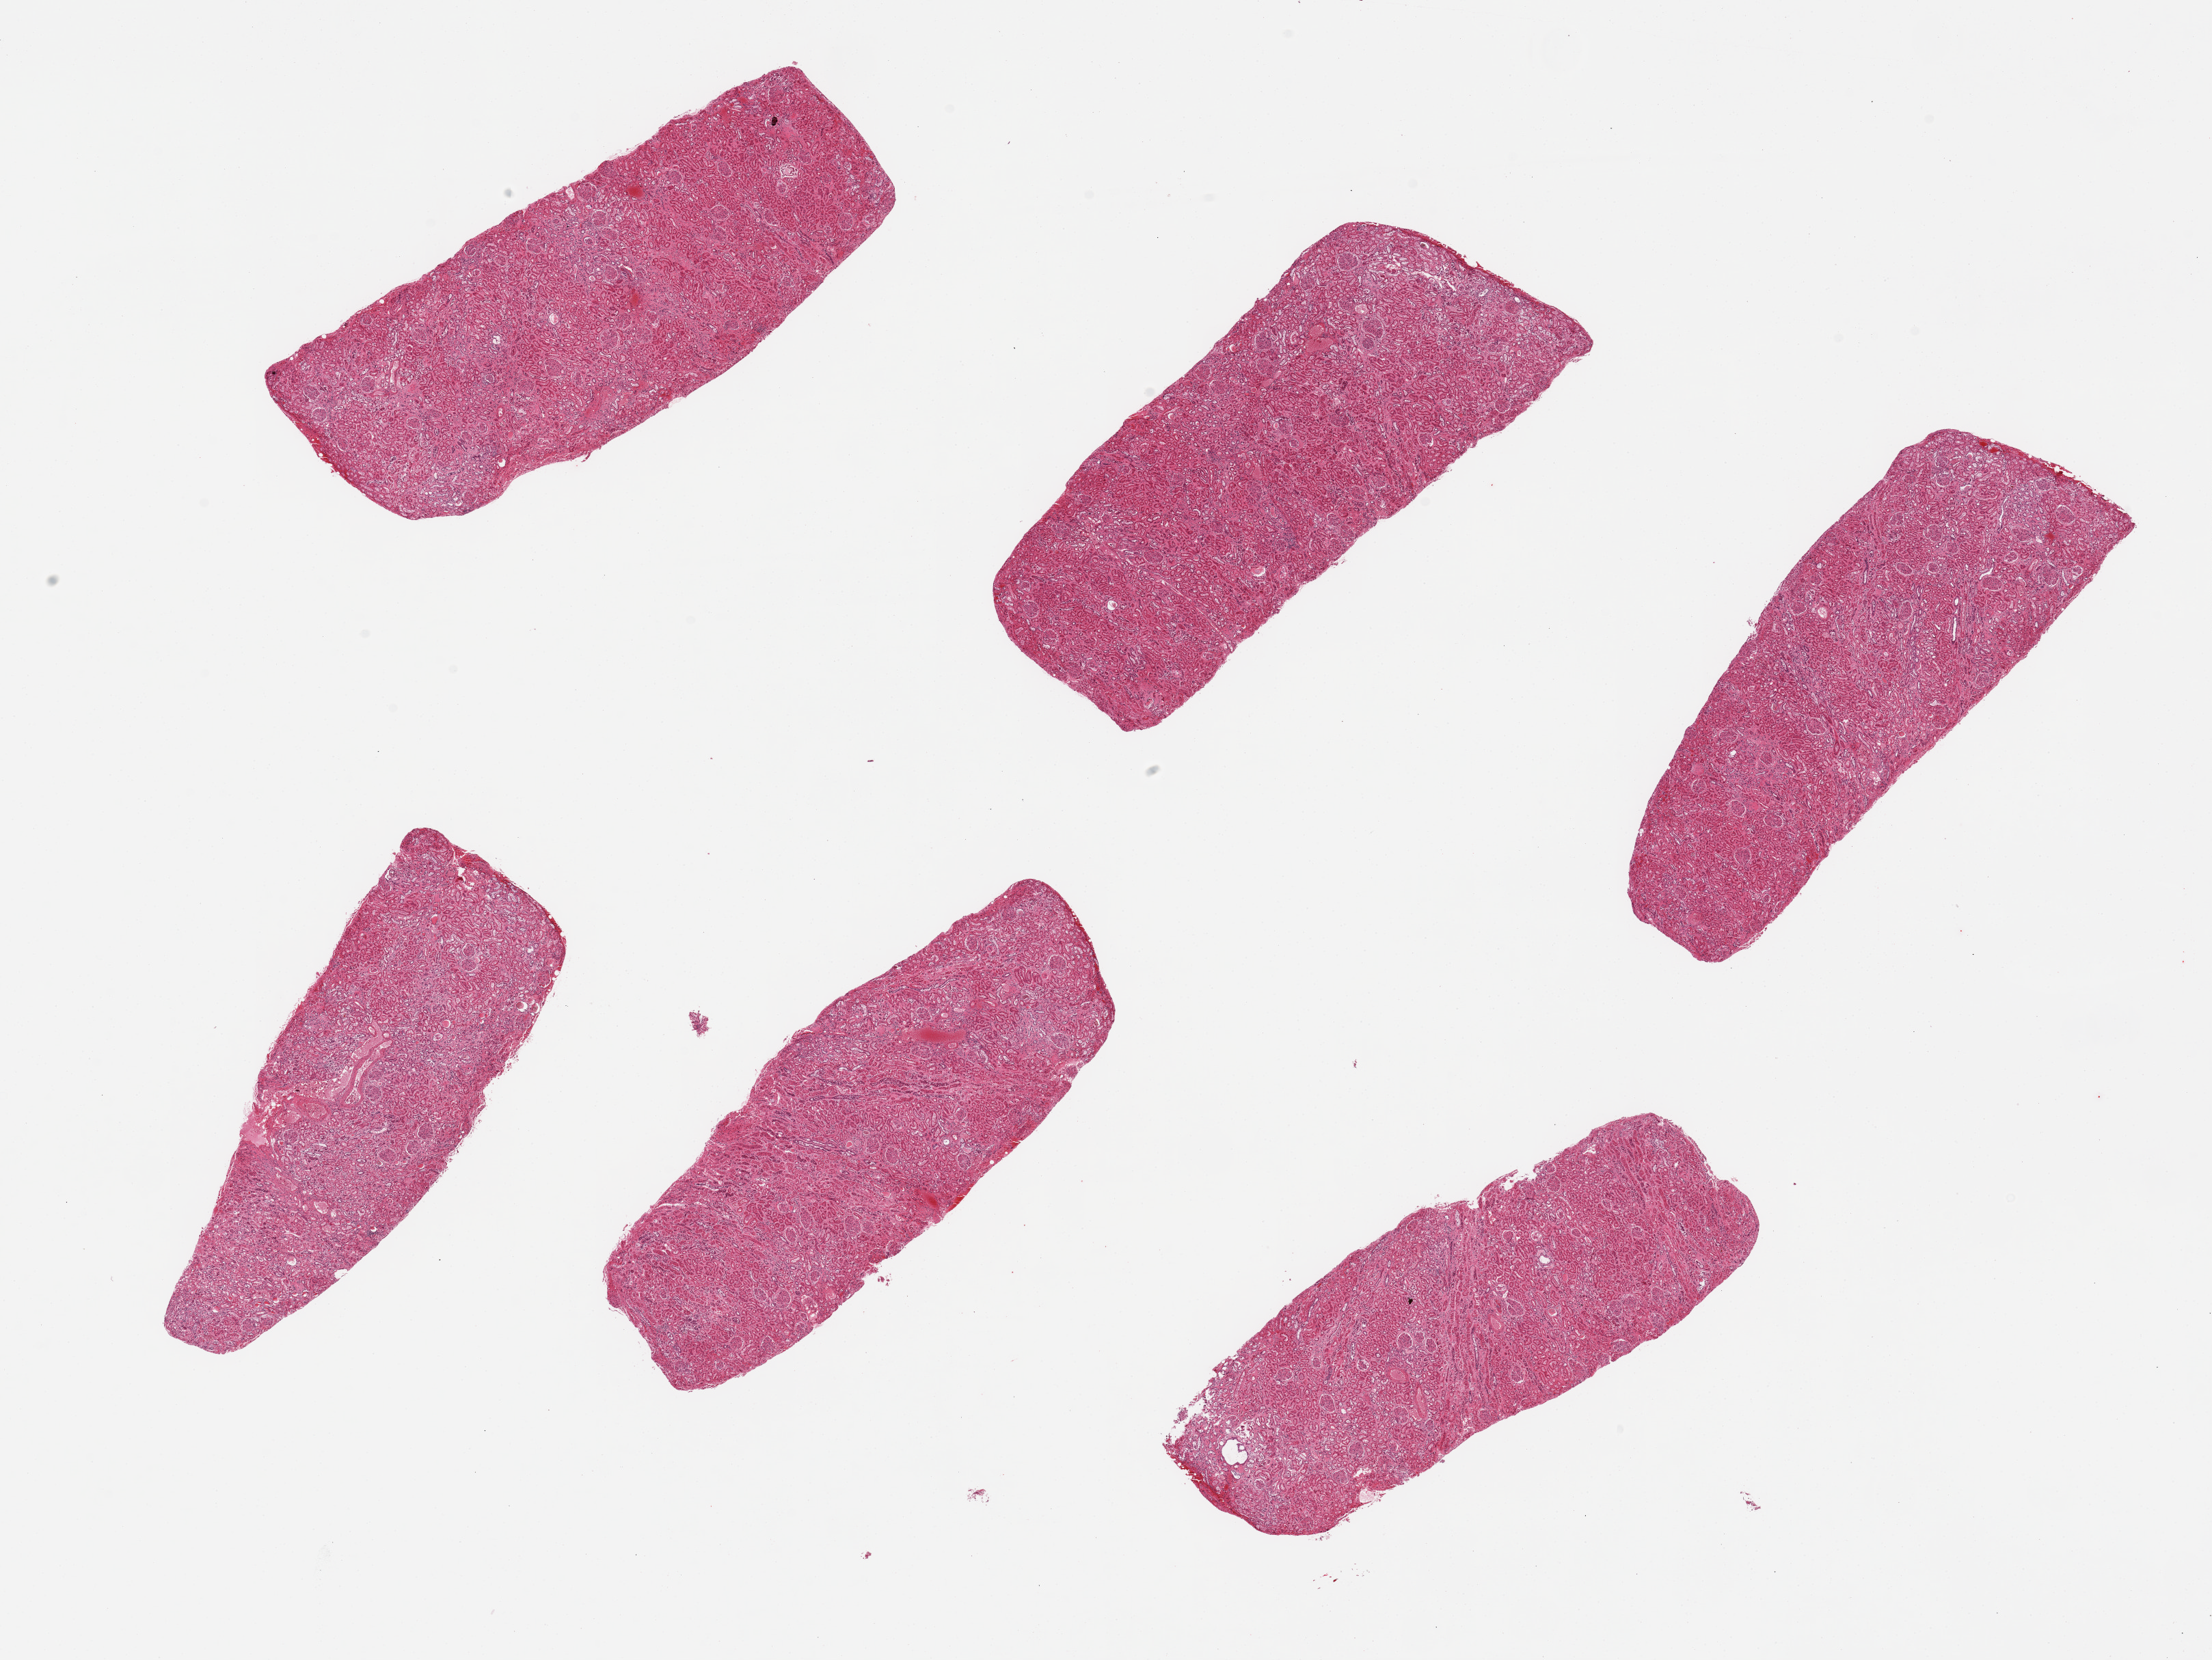
Hematoxylin and eosin (H&E) whole-slide image, brightfield — shown as a low-resolution overview of the whole scanned area (about 25.6 x 19.2 mm, from a 20x scan). PAXgene-fixed, paraffin-embedded tissue. Section of renal cortex (target tissue). Tissue donor sample.
Review note (as recorded): 6 pieces.